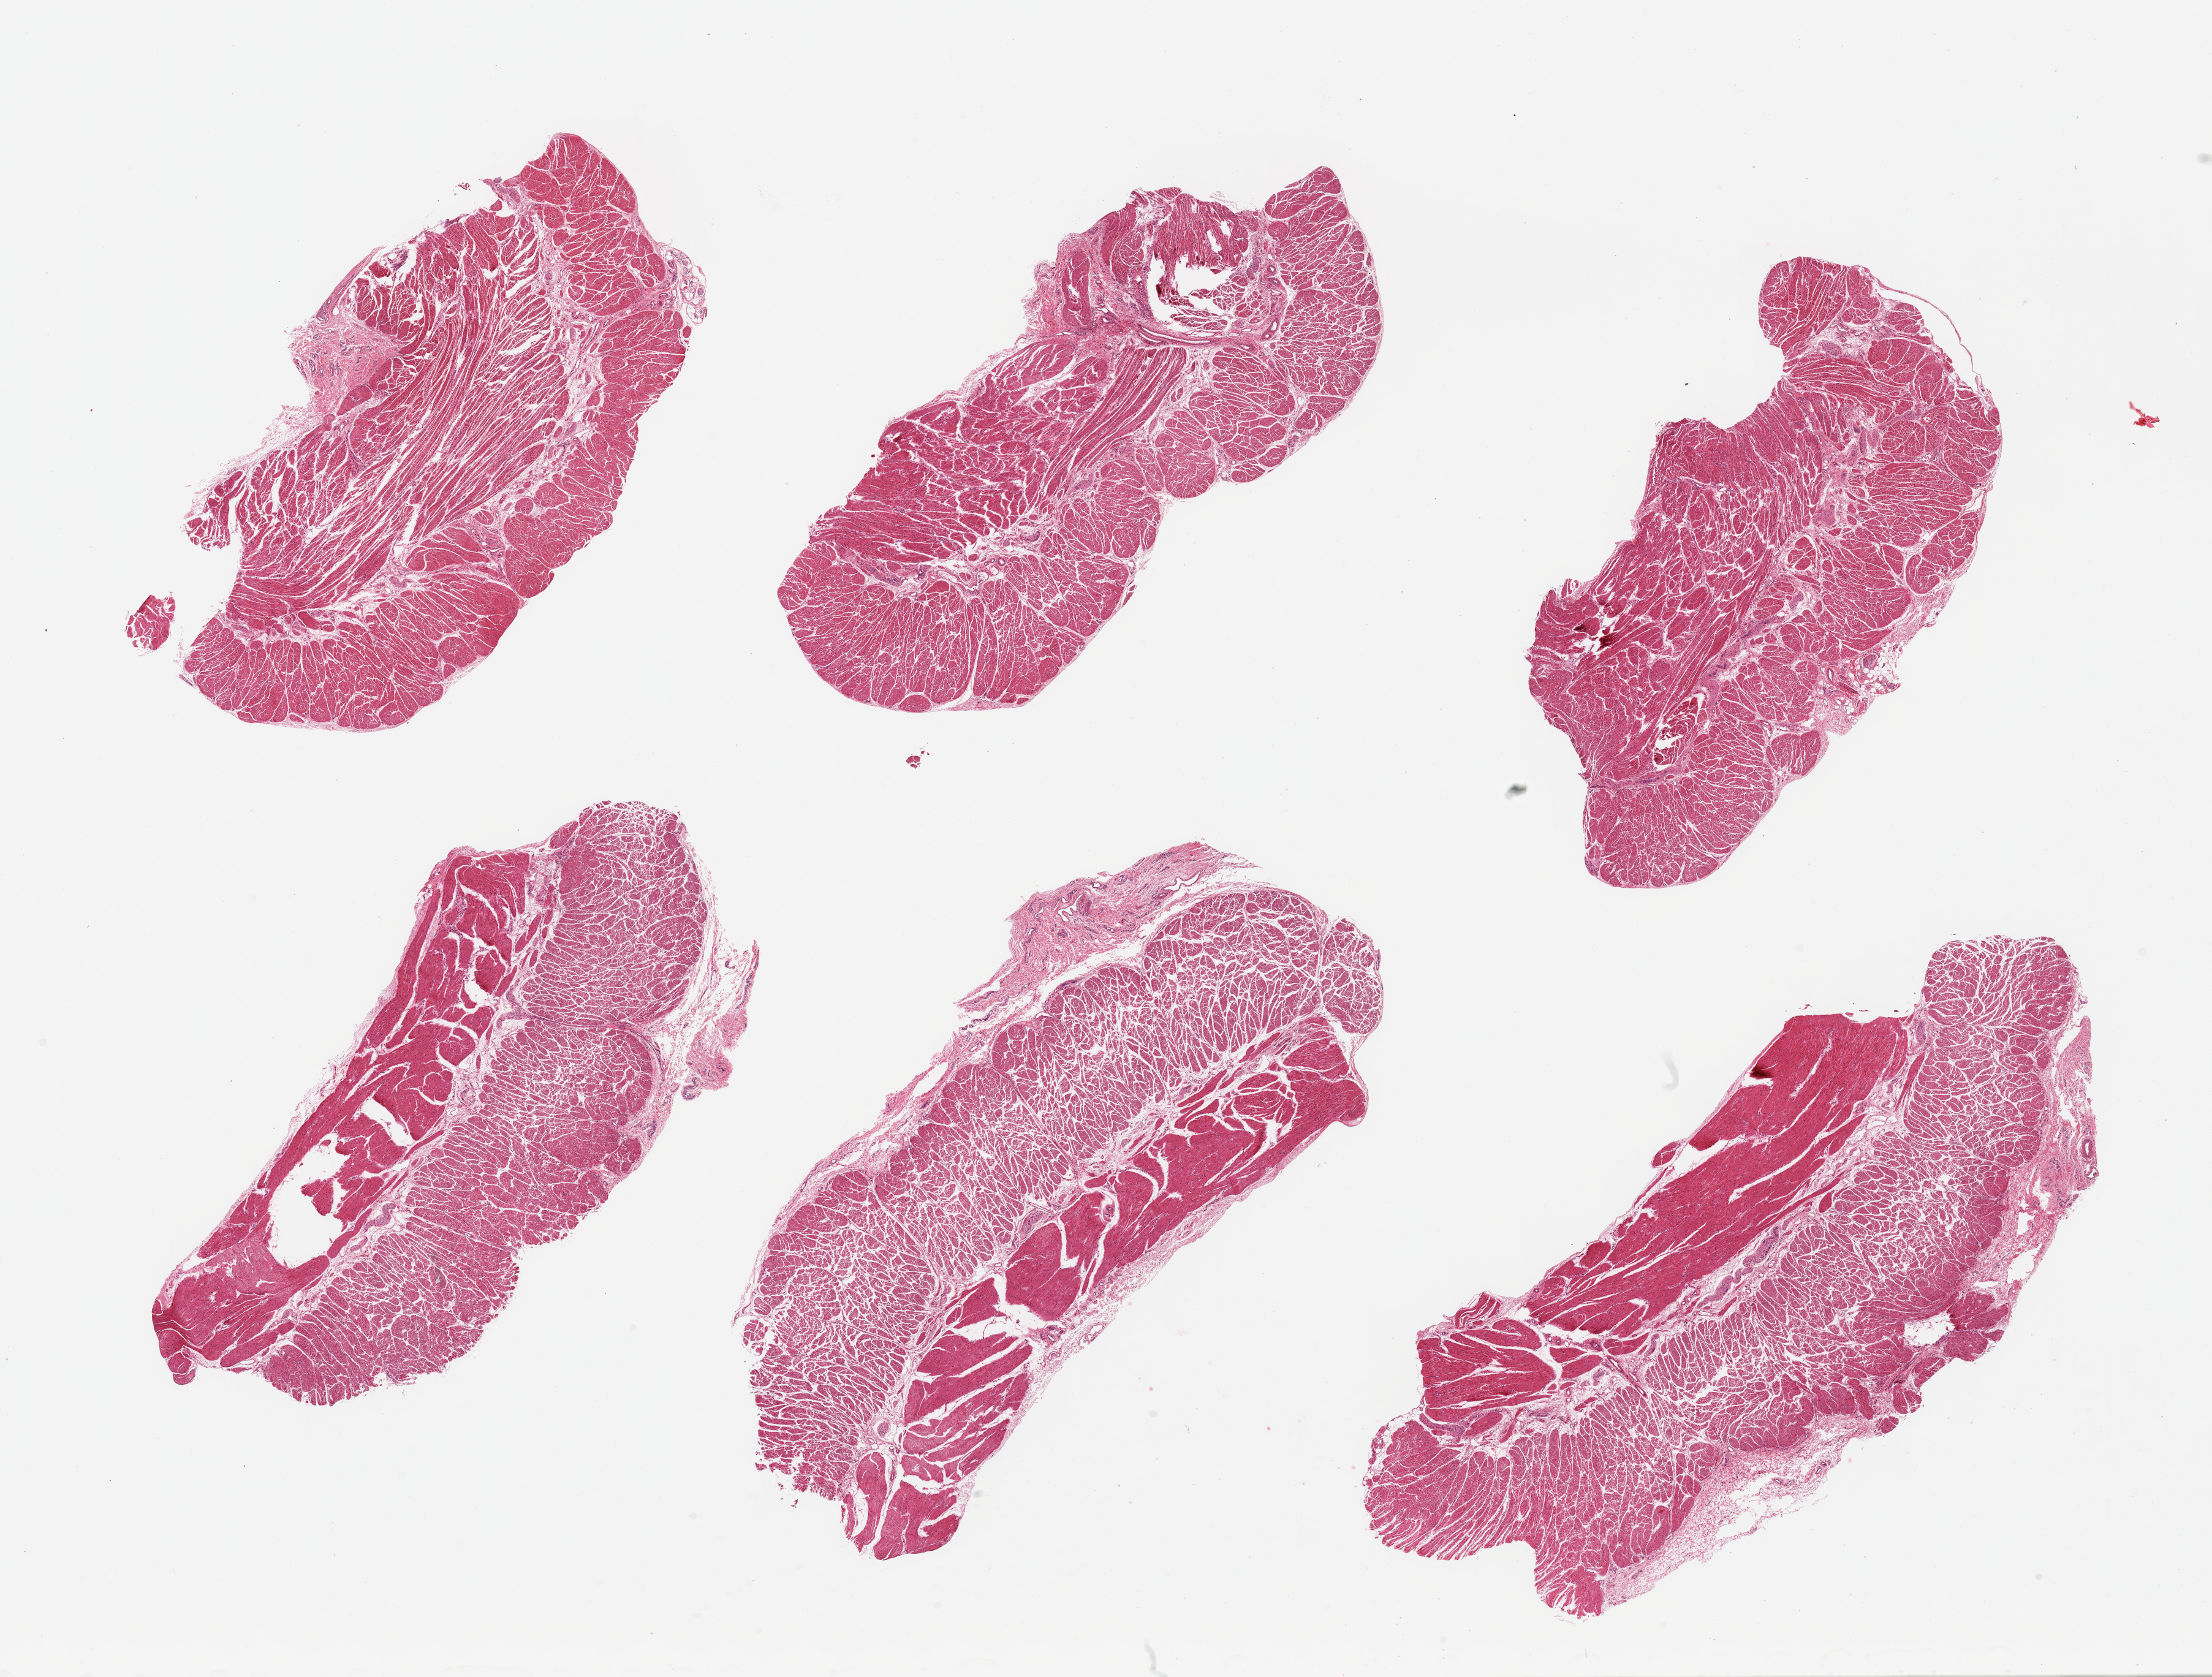
H&E whole-slide image, a low-resolution overview of the entire scanned area, about 28.5 x 21.6 mm. PAXgene-fixed, paraffin-embedded tissue. Target tissue: gastroesophageal junction. Tissue donor sample. Donor: male.
- reviewer comment on this tissue sample: 6 pieces; well trimmed